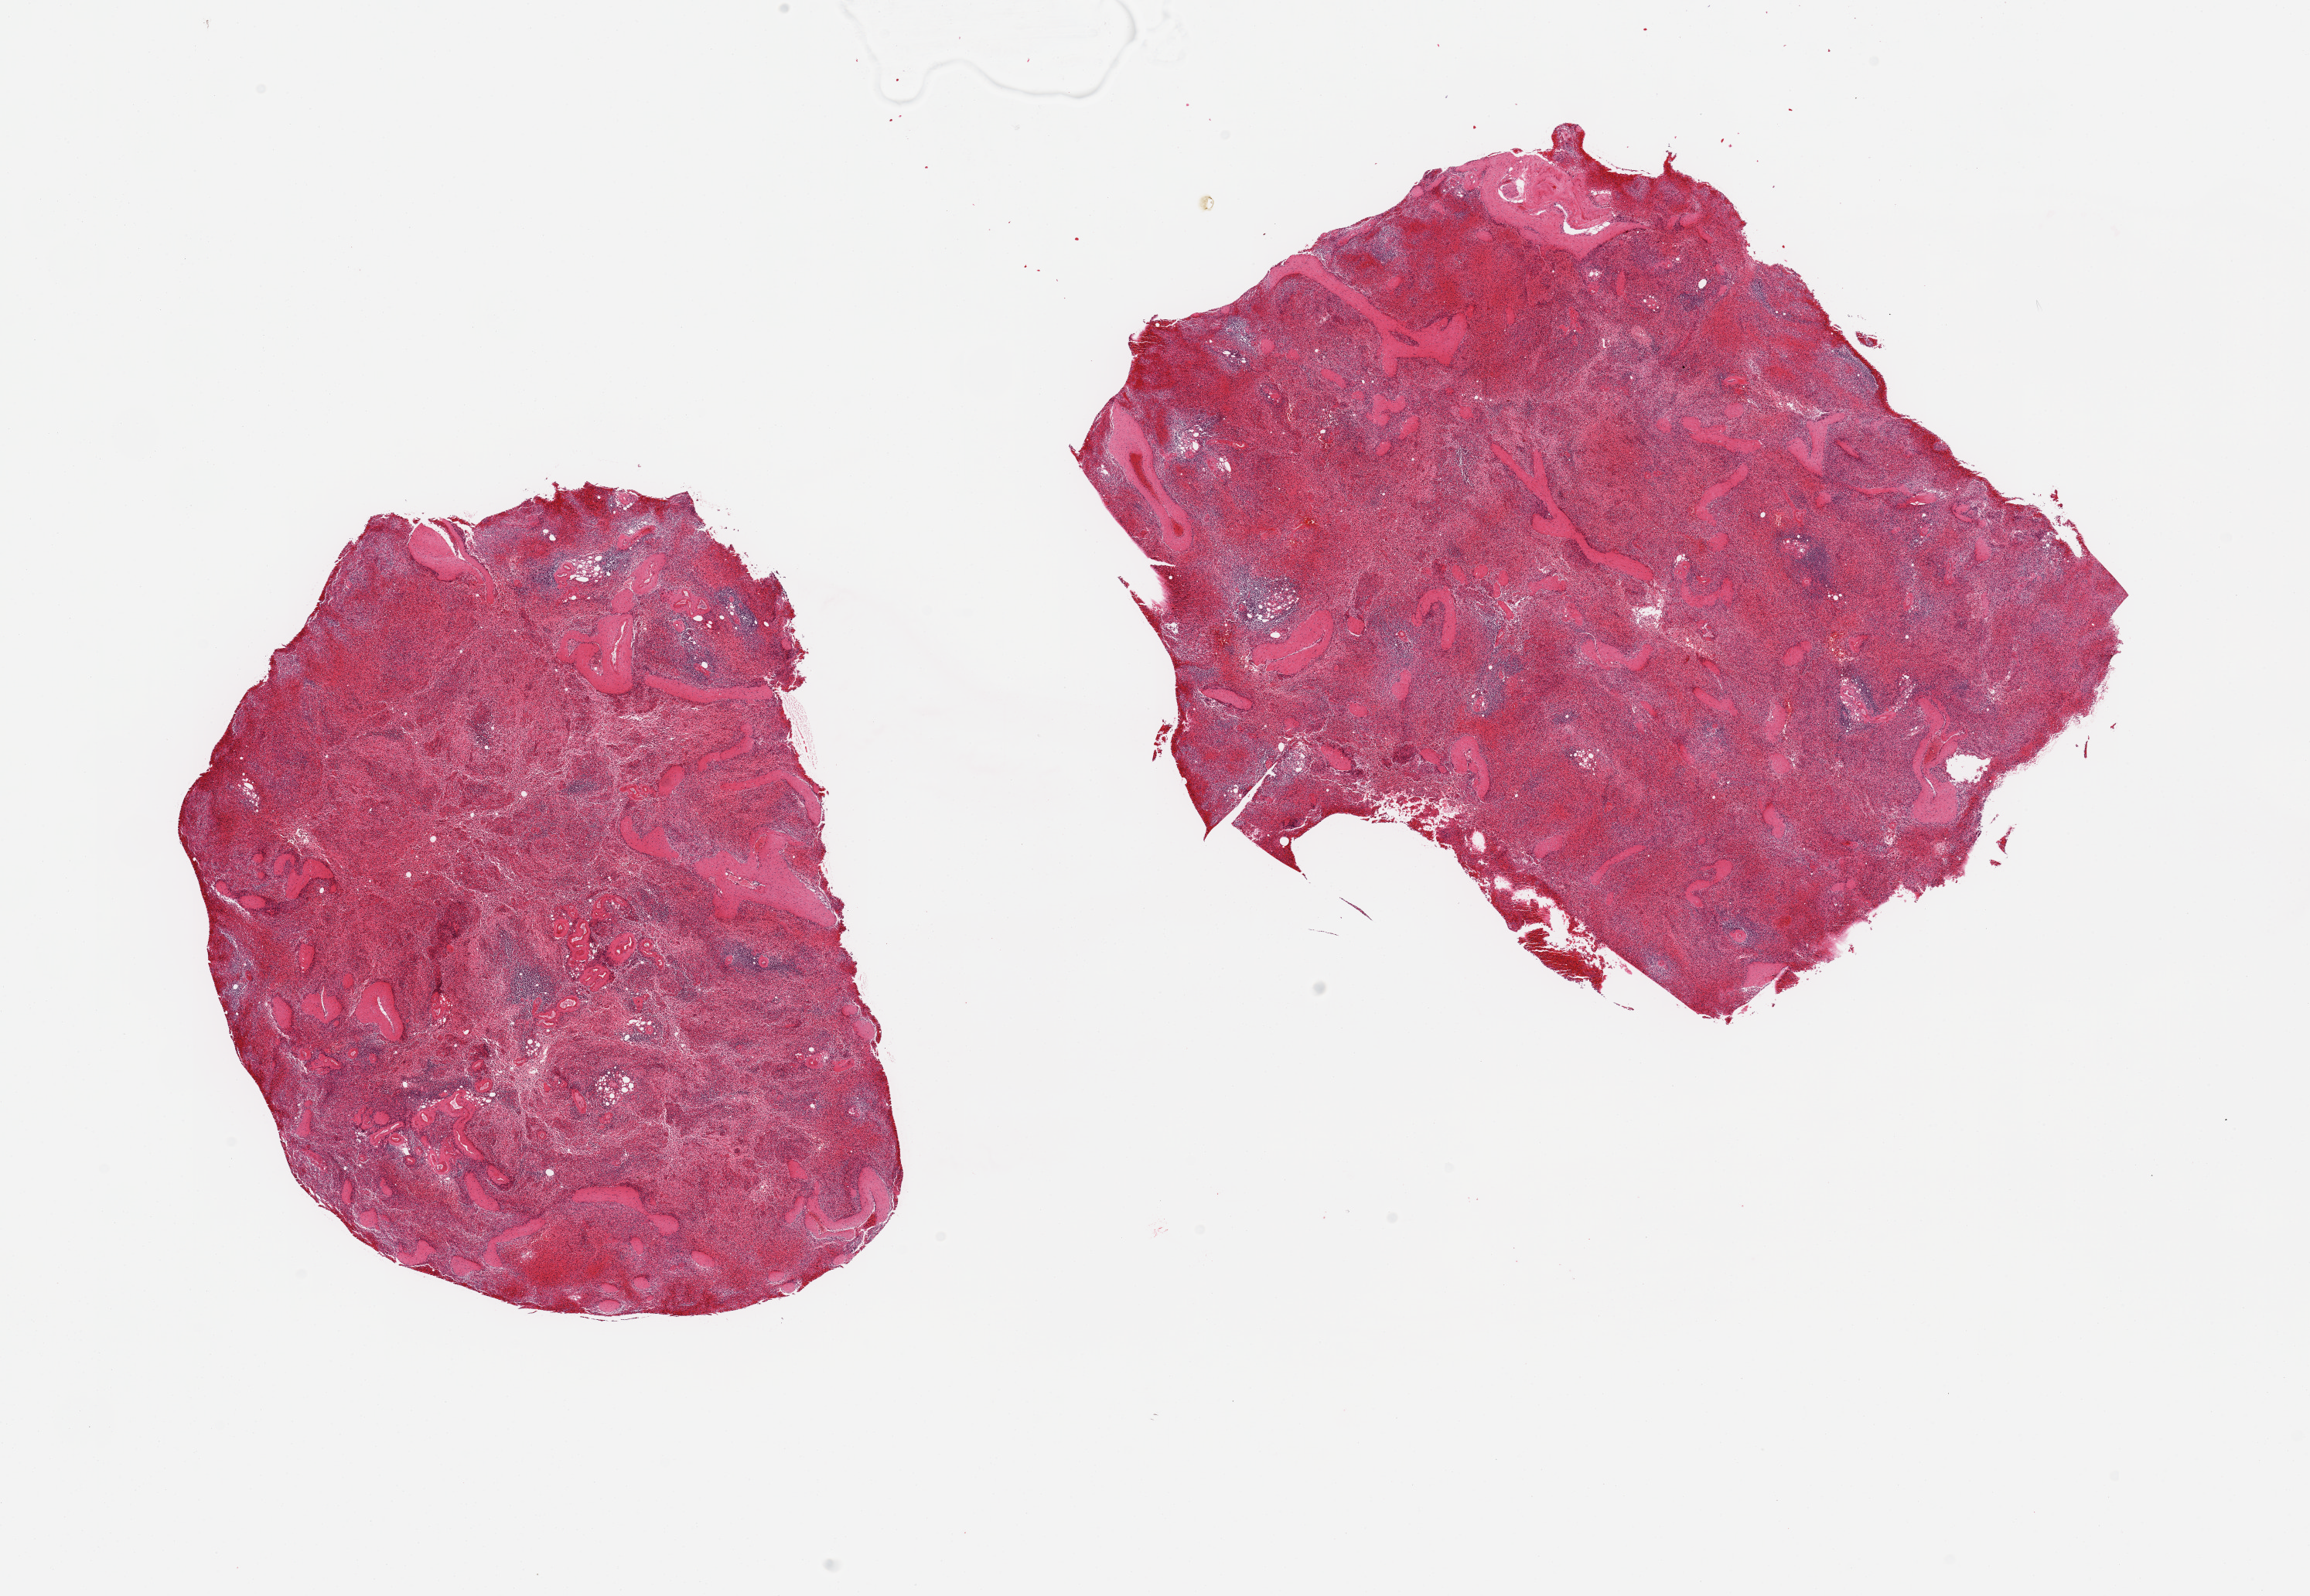
Whole-slide image, hematoxylin and eosin (H&E) stain — a low-resolution overview of the entire scanned area, about 23.6 x 16.3 mm (acquisition: 20x scan); PAXgene-fixed, paraffin-embedded tissue; section of spleen (target tissue); tissue donor sample.
• pathologist's review note for this sample: 2 pieces; congestion